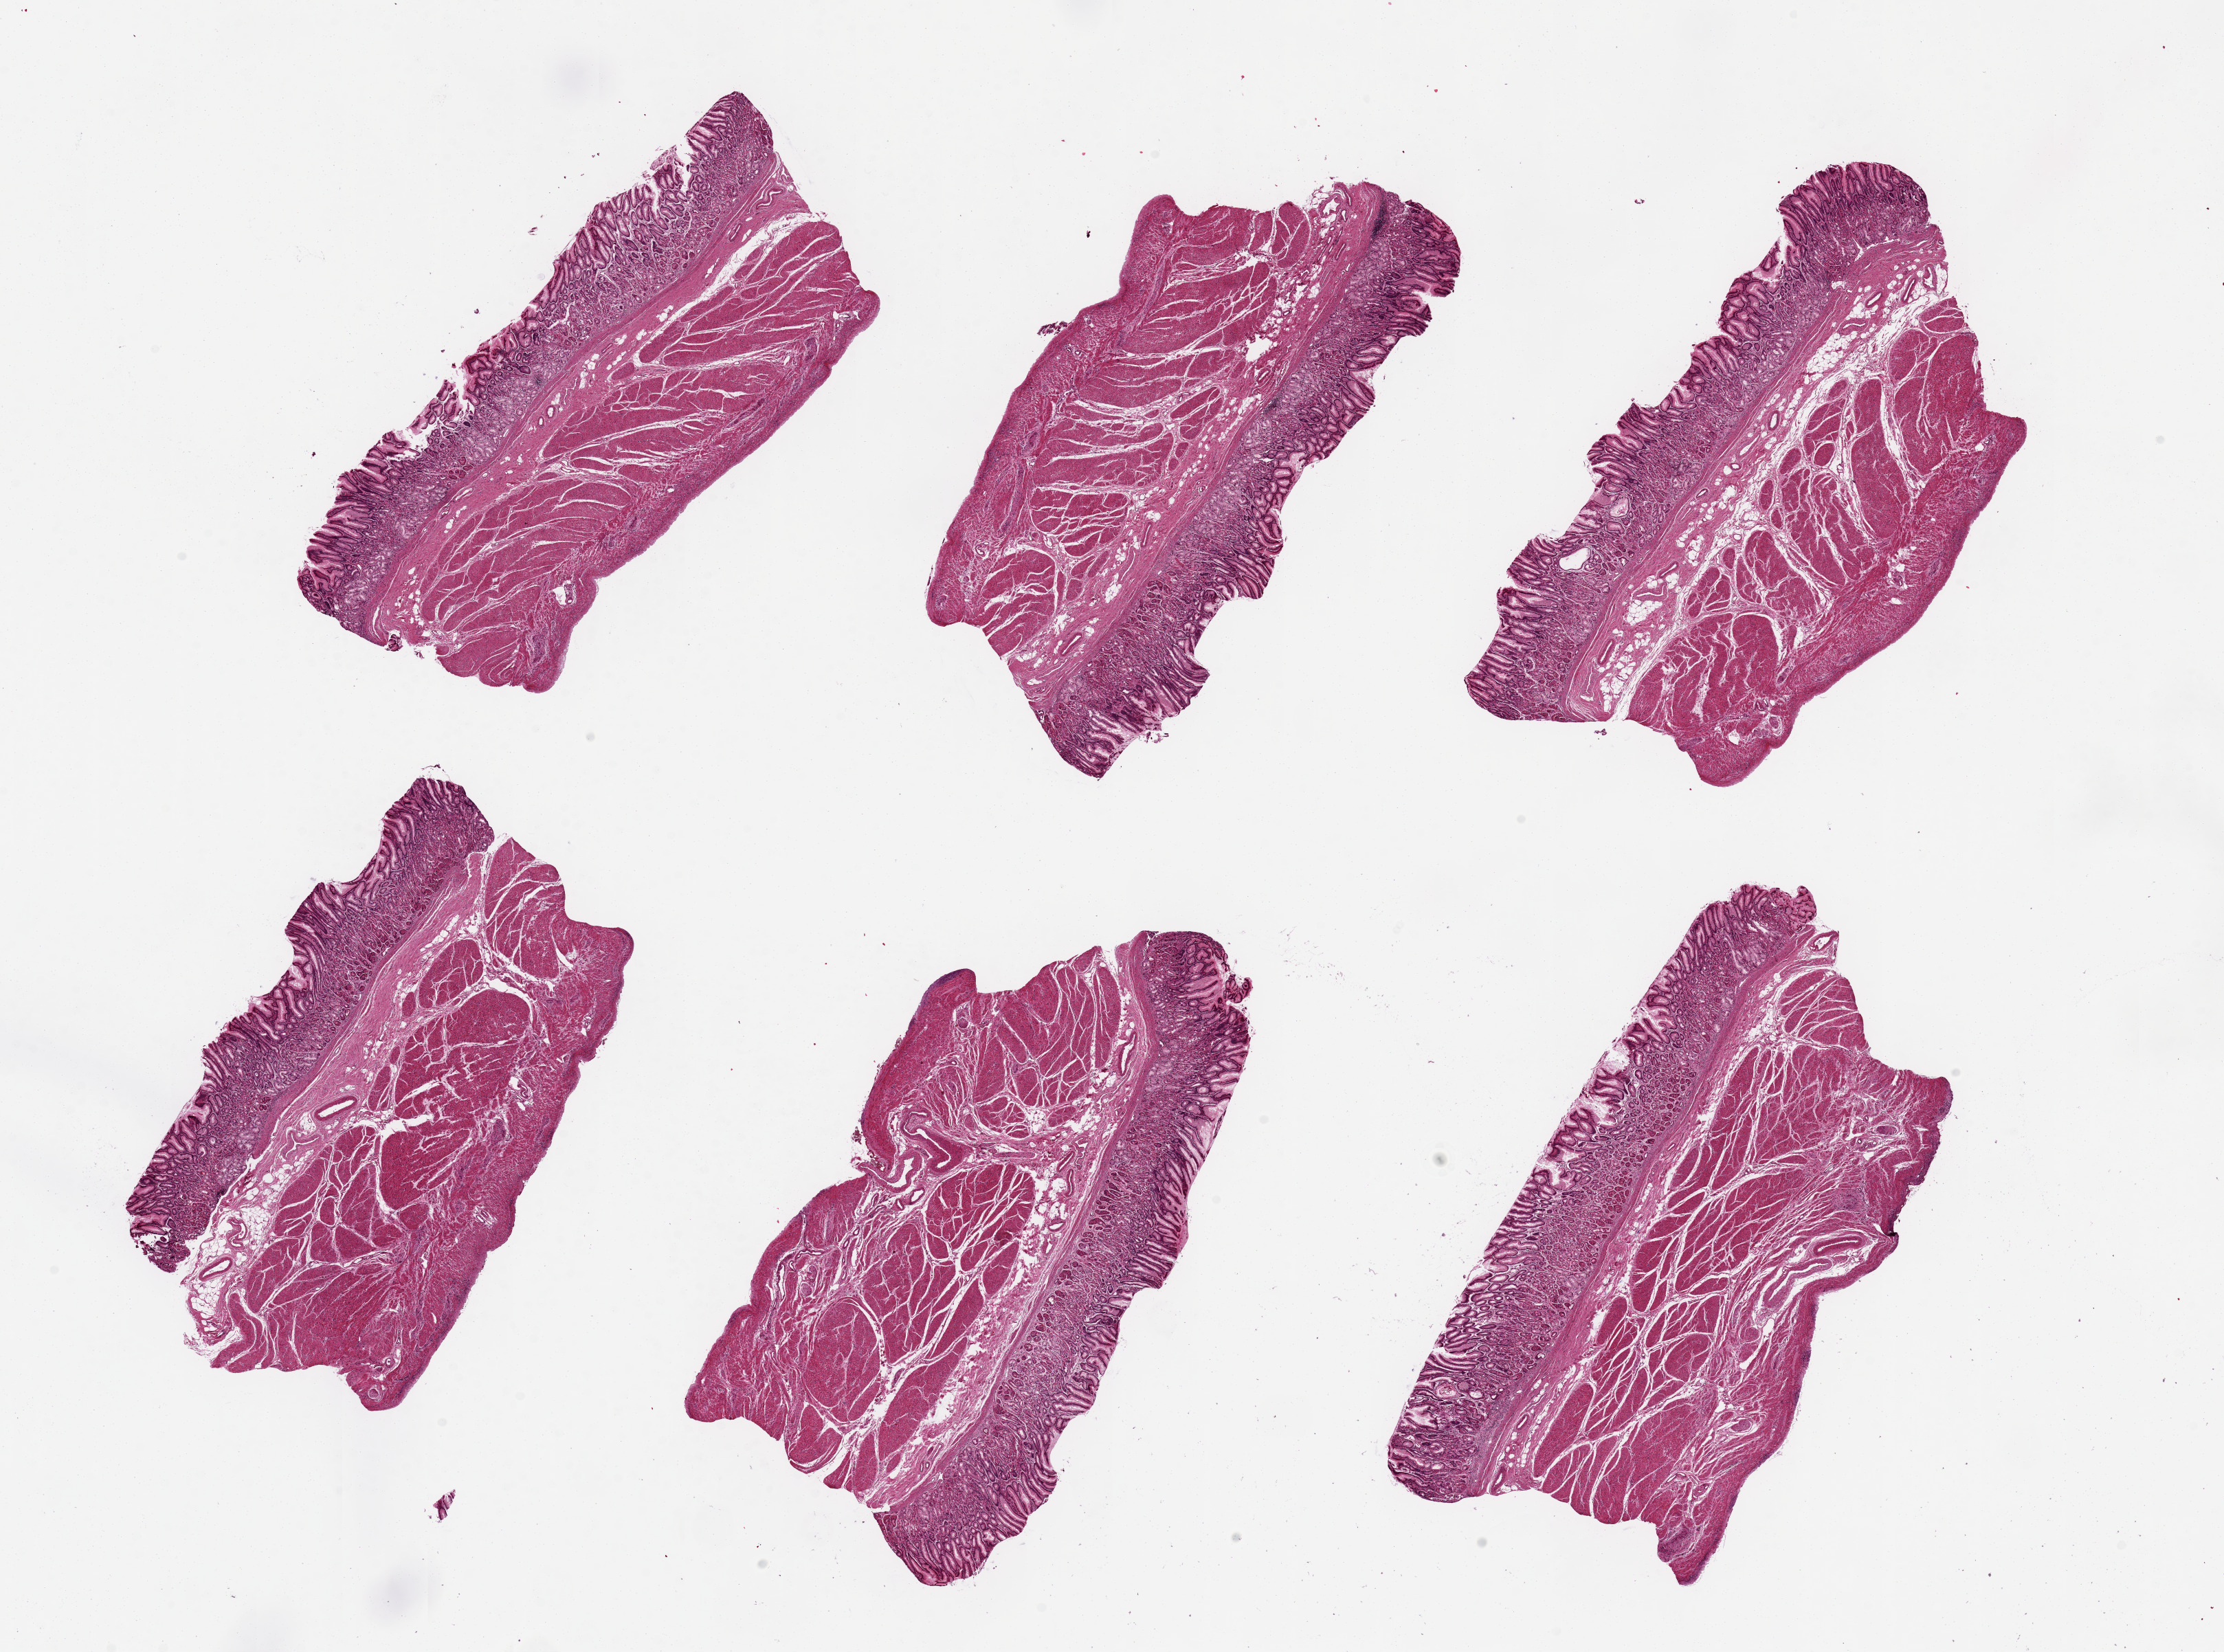
Hematoxylin and eosin (H&E) whole-slide image — shown as a low-resolution overview of the whole scanned area (about 25.6 x 19.0 mm, acquisition: 20x scan). PAXgene-fixed, paraffin-embedded tissue. Sampled site (target tissue): stomach. Donor tissue sample. Donor sex: male.
Pathologist's review note for this sample: 6 pieces, mucosa well-preserved, ~25% of thickness.